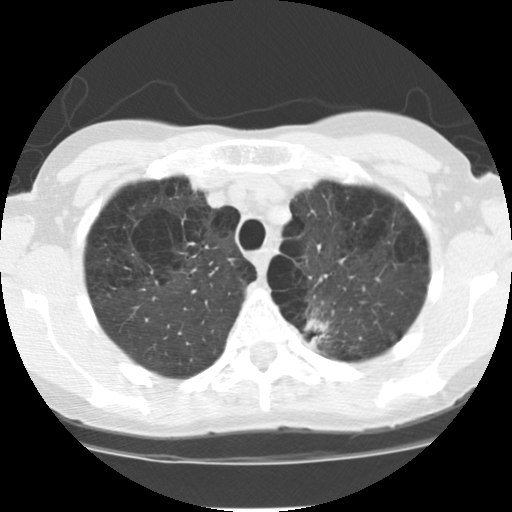
Axial slice from a low-dose chest CT screening exam, first (baseline) screen, lung window (W 1500 / L -600 HU), 512 × 512 image matrix, field of view 300 × 300 mm. Female participant, aged 61 years at enrolment. Current smoker at enrolment.
Expert reader's lesion annotation, box from (x=285, y=305) to (x=345, y=363) px. The screening reader recorded 4 non-calcified nodules or masses ≥4 mm on this exam (left upper lobe, right lower lobe, right middle lobe, left lower lobe); which of them this box marks is not recorded. Official screen result: positive, change unspecified: nodule(s) >= 4 mm or enlarging nodule(s), mass(es), or other non-specific abnormalities suspicious for lung cancer. Lung cancer was diagnosed 68 days after this screen: adenocarcinoma, NOS, left upper lobe, poorly differentiated (G3), stage IB (AJCC 6th edition), 17 mm at pathology.